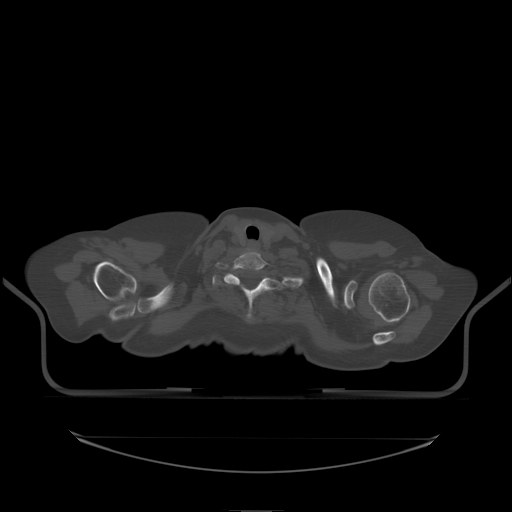
CT including the spine, one axial slice; position 189 of 242 along the scan axis; bone window (W 1800 / L 400 HU); 2.5 mm slice thickness; 512 × 512 image matrix, field of view 500 × 500 mm. Patient: female, 53 years. From the clinical record (not read from this slice): primary cancer: lung.
Outlined on this slice (semi-automatically segmented with operator editing):
- T1 vertebra: bounding box <214,274,284,321> (left, top, right, bottom; pixels)